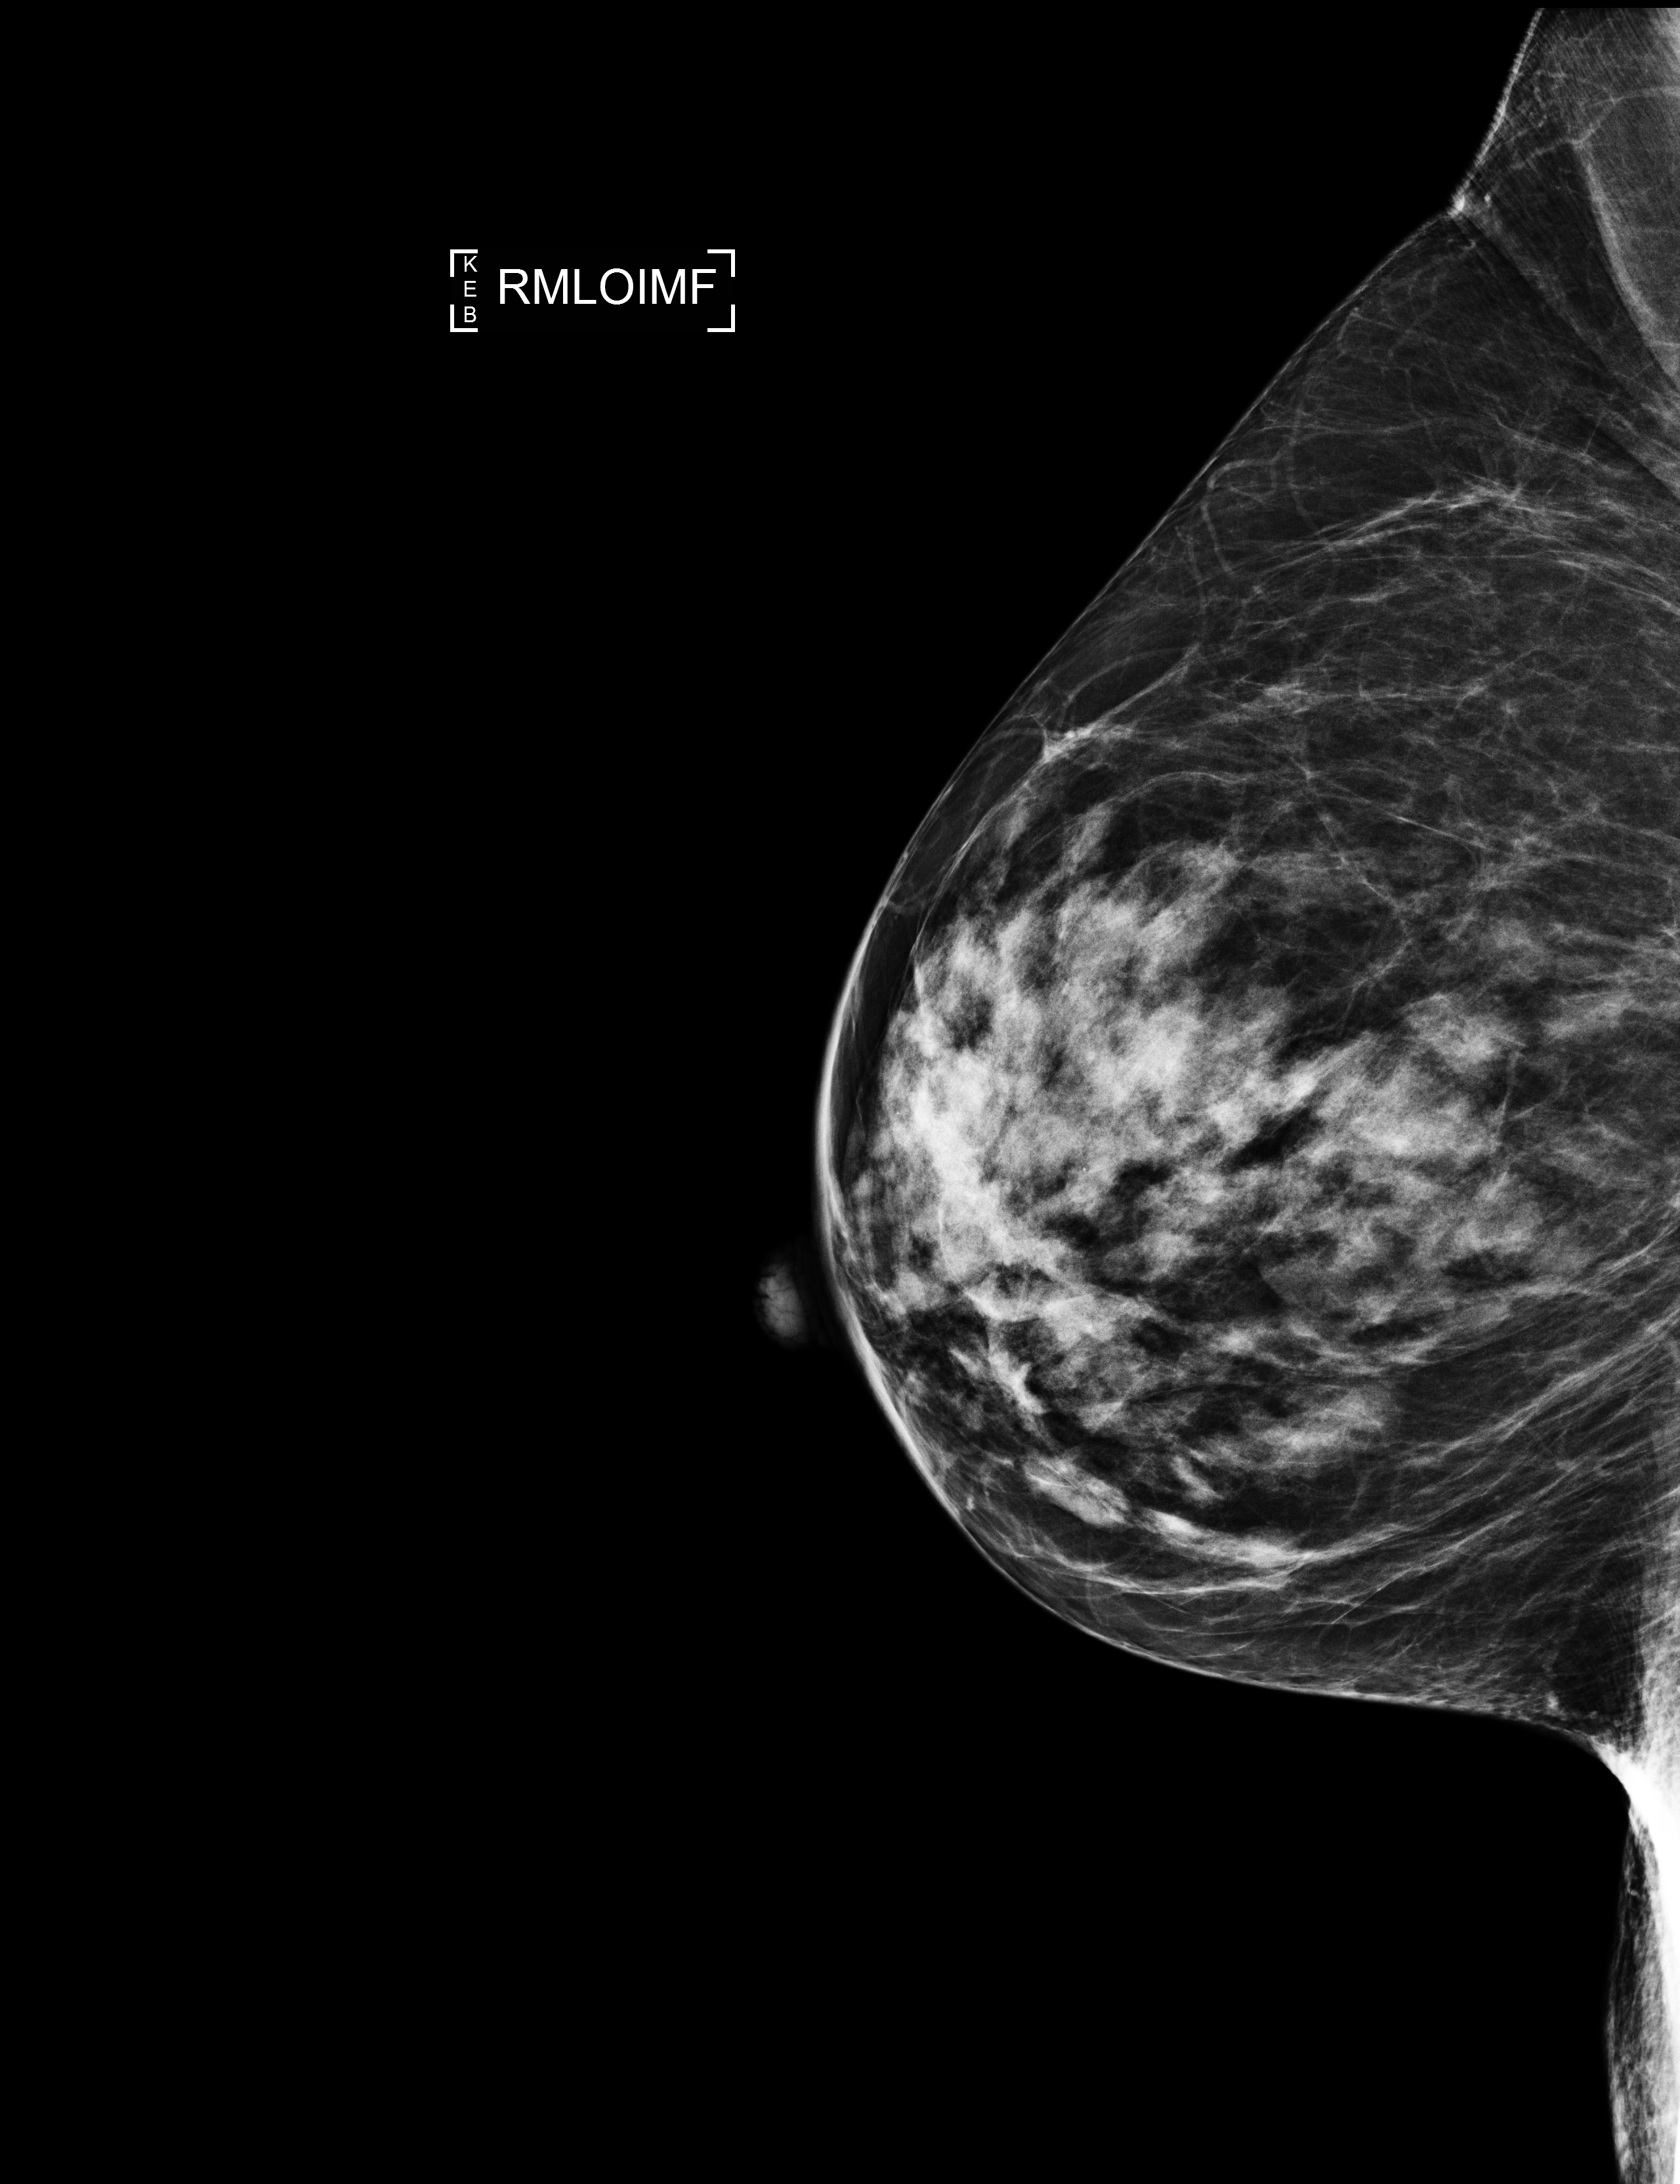
Full-field digital mammogram (FFDM), right breast, mediolateral oblique (MLO) view (infra-mammary fold), screening examination, compressed breast thickness 54 mm. Female patient, age 72 years.
Breast density at the screening exam (both breasts): heterogeneously dense (BI-RADS density category c). Final BI-RADS assessment for this screening round (tomosynthesis exam, both breasts): category 1. Recall: no recall after this screen.